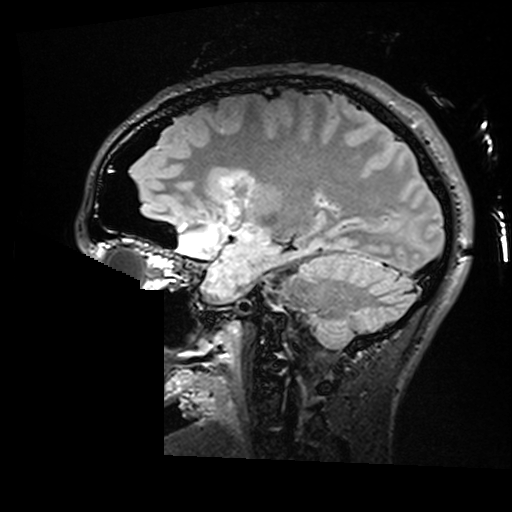
Brain MRI from a brain-tumour surgery series, one sagittal slice. Position 105 of 176 along the scan axis. T2 FLAIR. 1 mm slice thickness. 512 × 512 image matrix. Case-level facts recorded for this patient, not image findings: histopathology: Astrocytoma; WHO grade: 2; IDH mutation: yes; tumour location: Right Insular.
Outlined on this slice (expert manual segmentation):
- residual tumour: bounding box (x1, y1, x2, y2) in pixels: (219, 170, 244, 188)